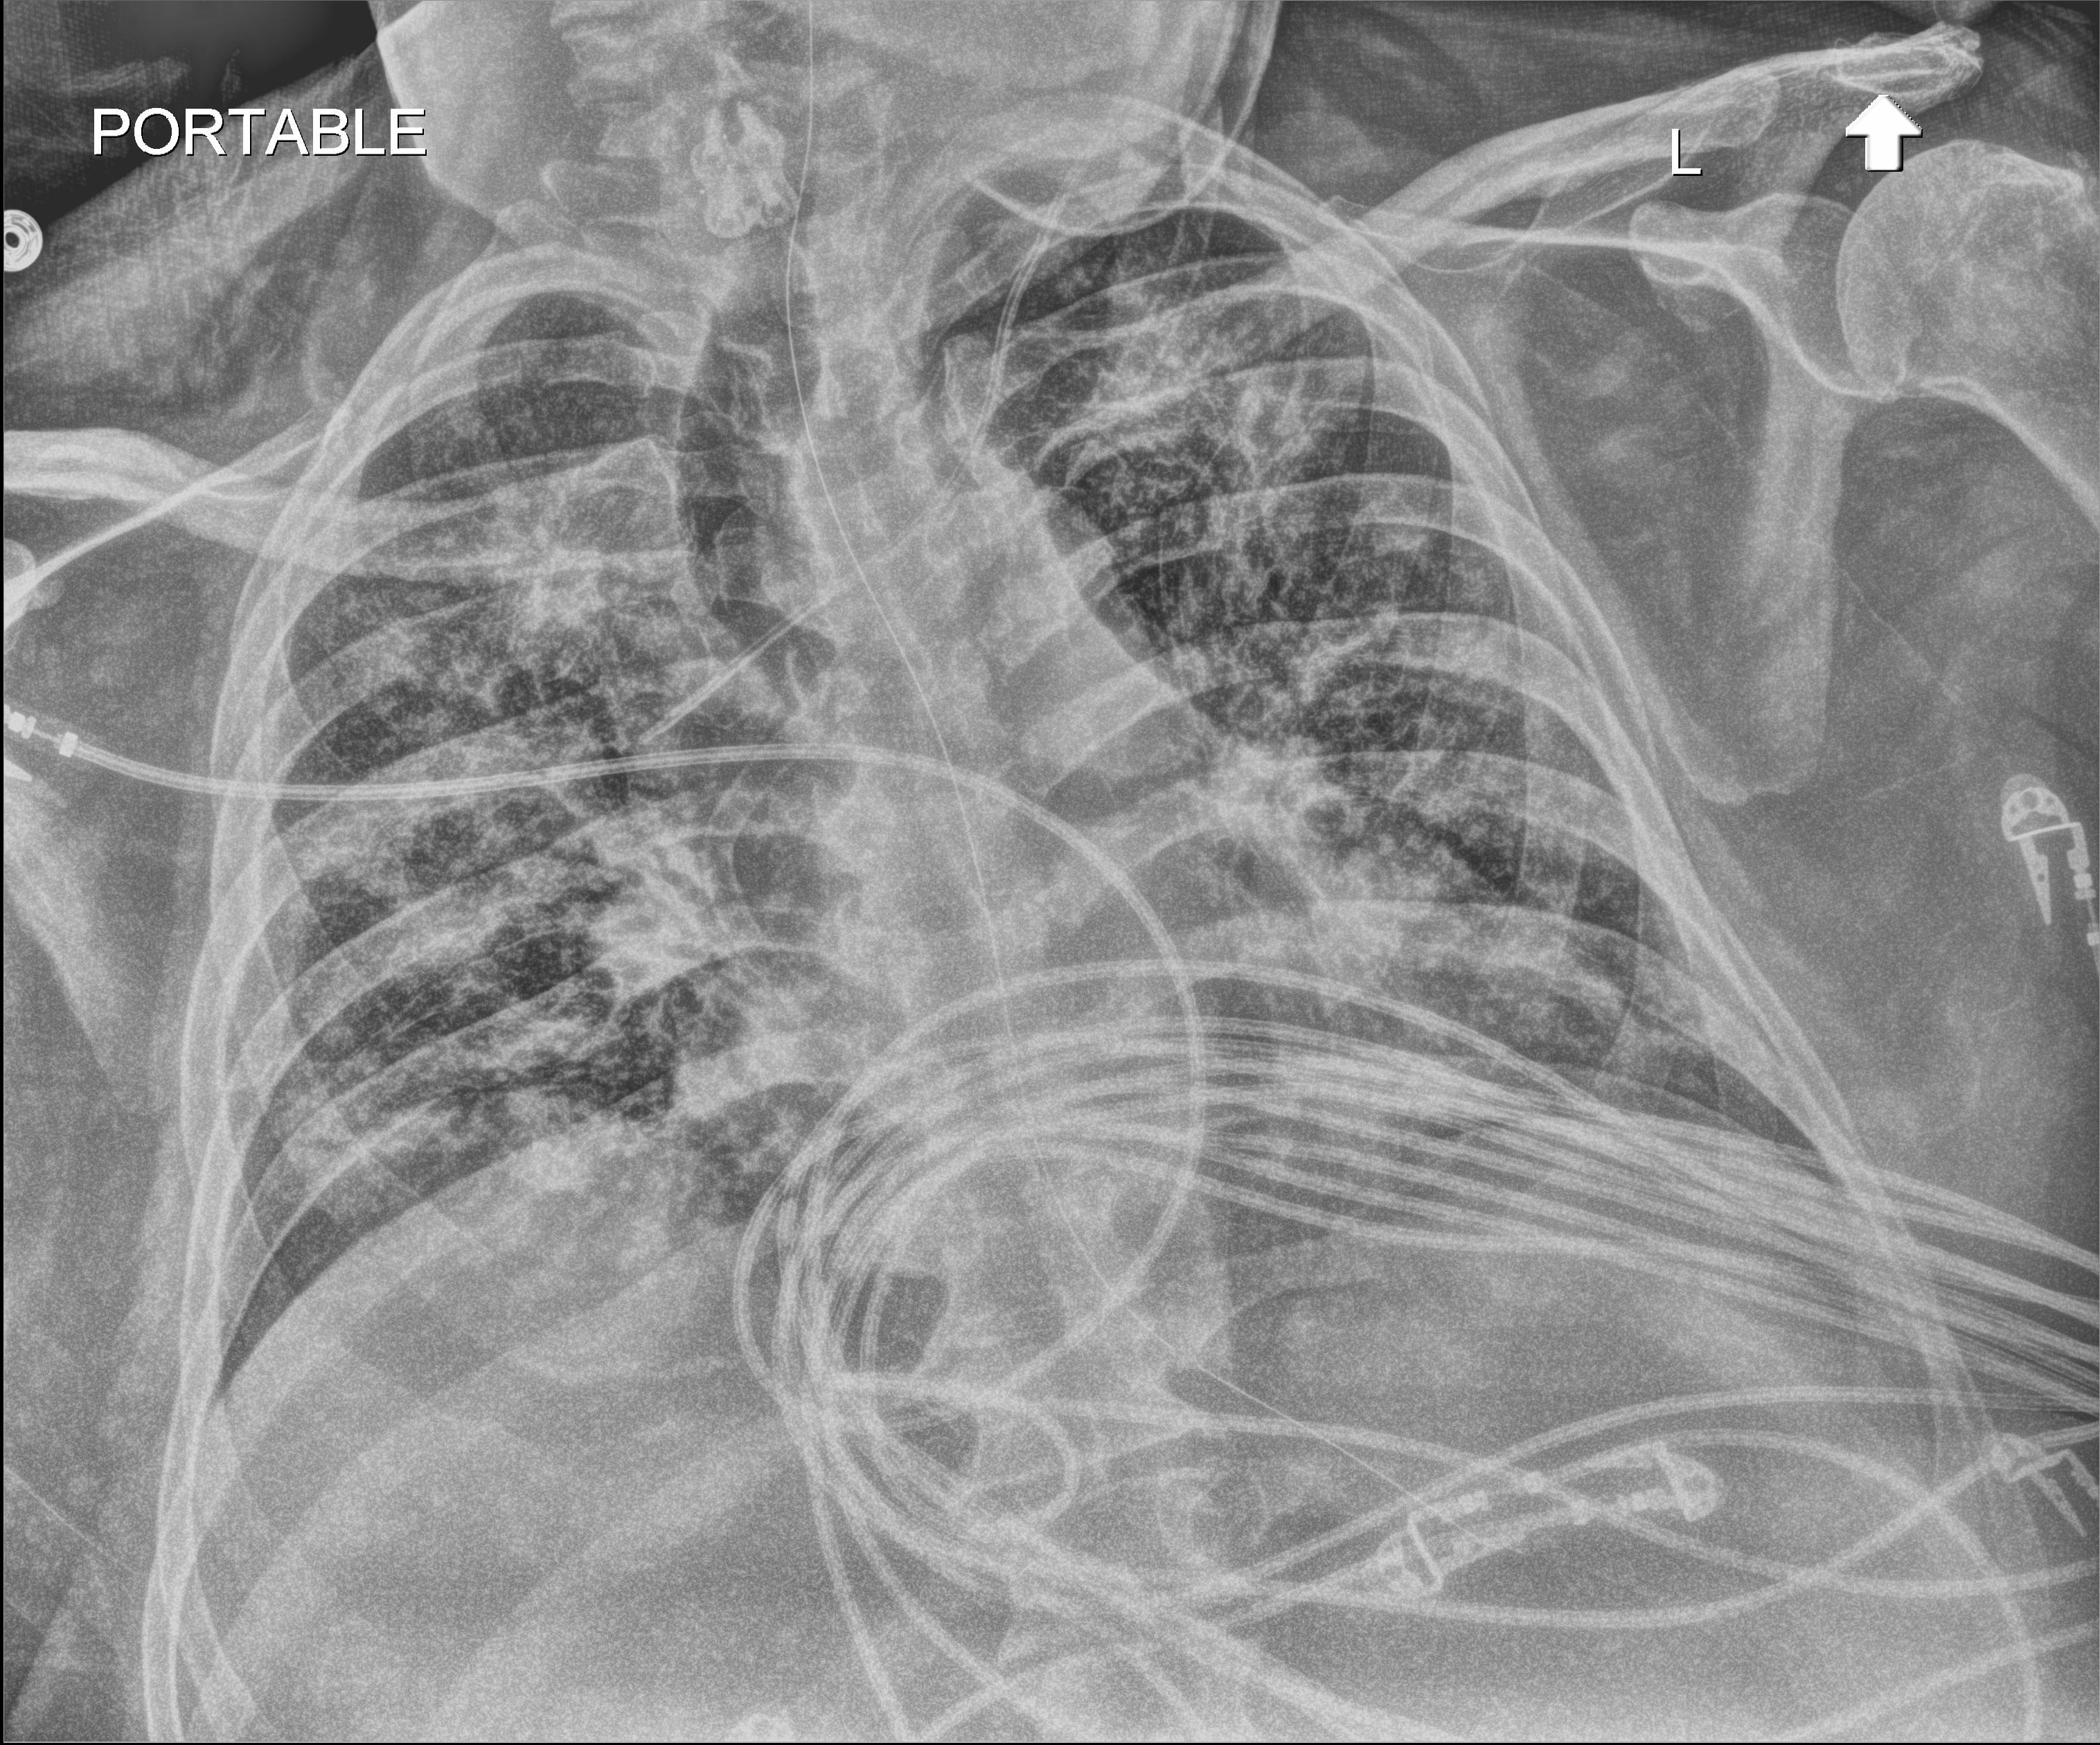
Chest X-ray; anteroposterior (AP) projection. Male patient hospitalised with COVID-19, age 18–59 years.
From the hospital-stay record, not from the radiograph (when in the stay this image was taken is not recorded):
- length of hospital stay: 47 days
- diabetes (admission record): no
- COPD (admission record): no